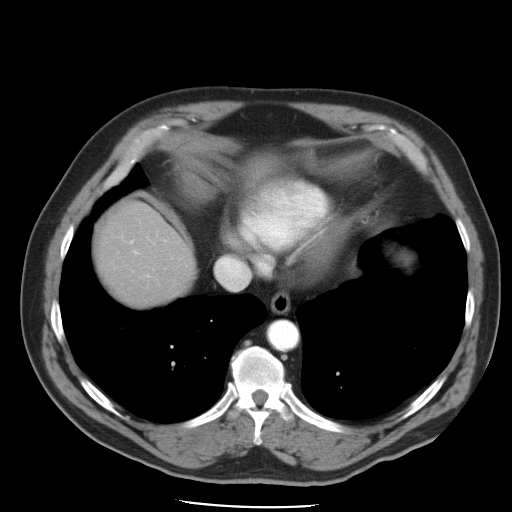
Contrast-enhanced abdominal CT, one axial slice; slice 43 of 49 in the series (ordered by position); reconstruction kernel STANDARD; 120 kVp; intravenous contrast given; soft-tissue window (W 400 / L 40 HU); 512 × 512 image matrix, field of view 395 × 395 mm. Male patient, age 68 years. Case-level facts recorded for this patient, not image findings: diagnosis: colorectal cancer liver metastases, imaged before liver resection; multiple liver metastases: yes; largest metastasis: 1.7 cm; chemotherapy before resection: yes.
Outlined on this slice (manually delineated by an expert):
- hepatic veins: box from (x=216, y=258) to (x=250, y=290) px
- liver: (x=99, y=203)–(x=194, y=304)
- planned liver remnant (the part of the liver to remain after resection): (x=99, y=203)–(x=194, y=305)
- portal vein (with intrahepatic branches): (x=130, y=241)–(x=149, y=278)